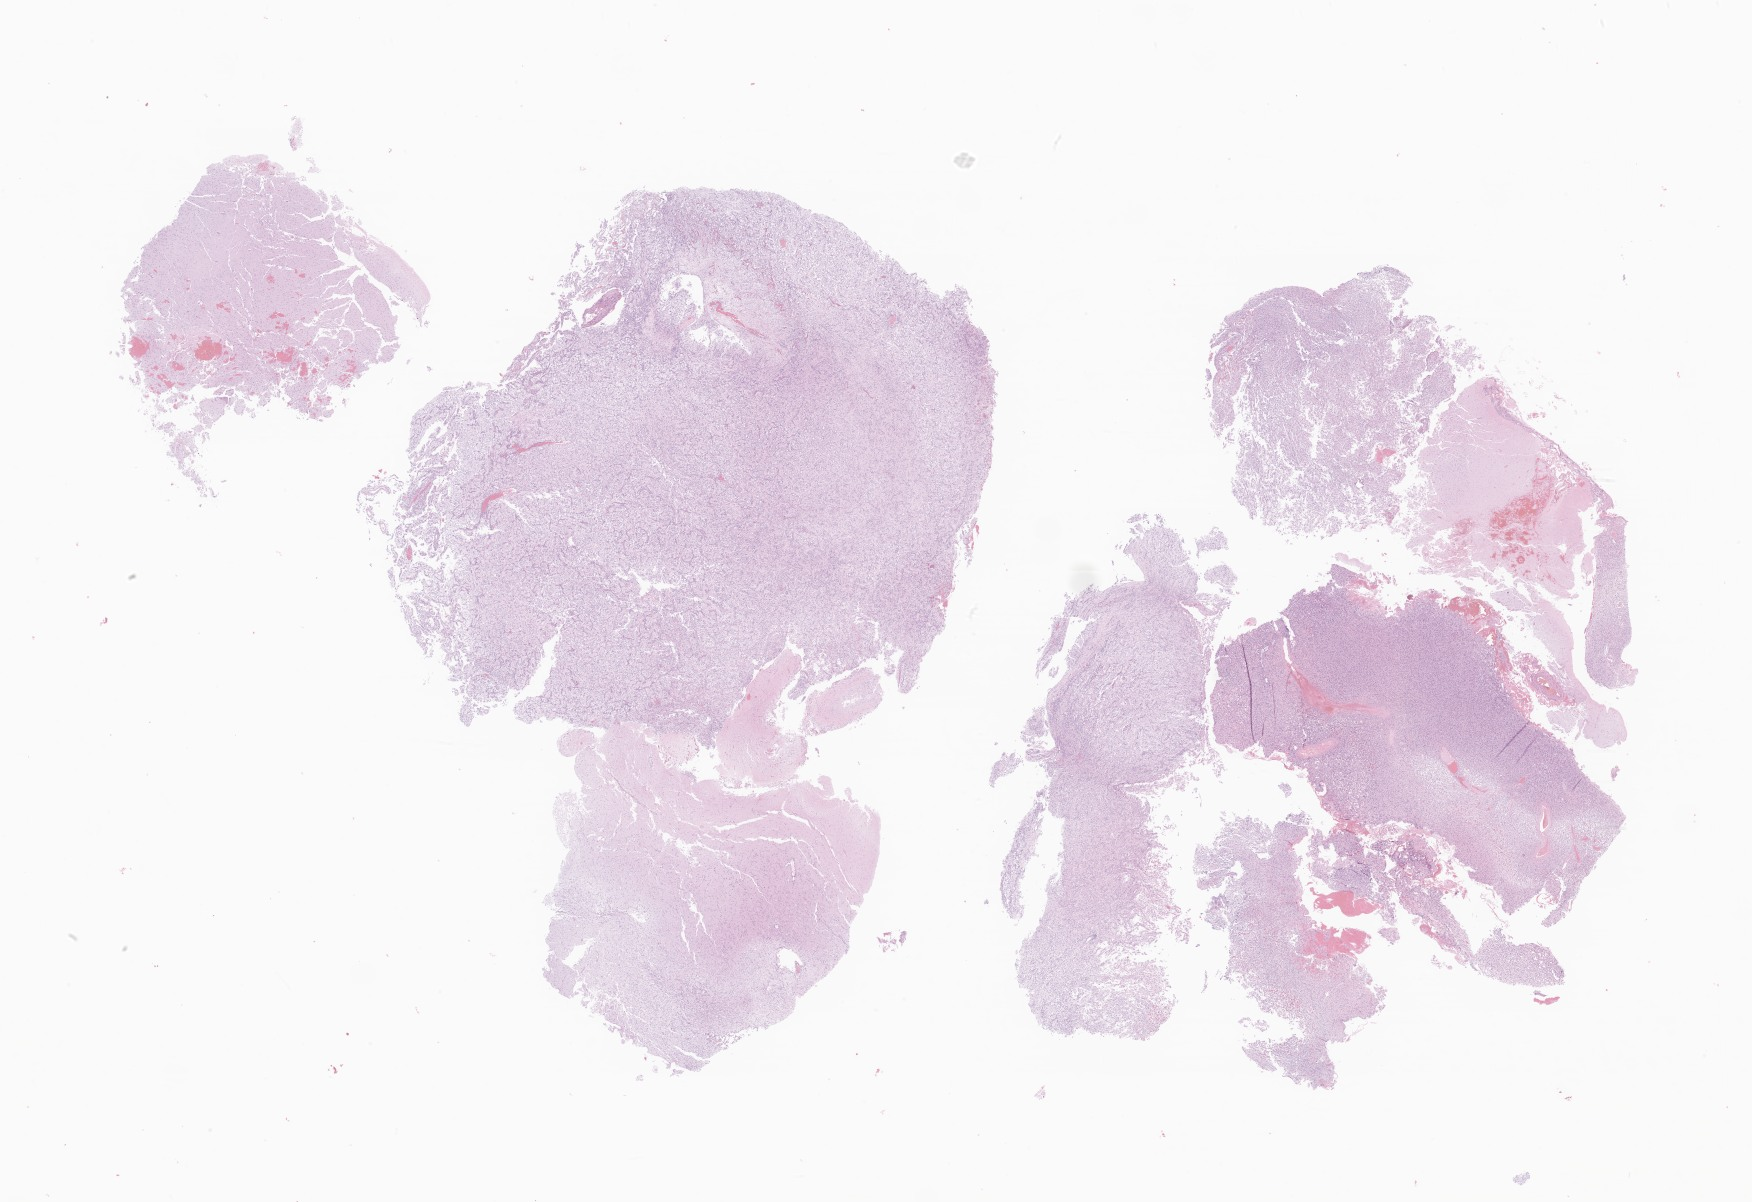
Whole-slide image, hematoxylin and eosin (H&E) stain of tumor tissue from the brain, a low-resolution overview of the entire scanned area, about 29.6 x 20.3 mm; formalin-fixed, paraffin-embedded (FFPE) tissue. Patient: male, age 403 days (about 1.1 years).
Diagnosis: Neoplasm, malignant.